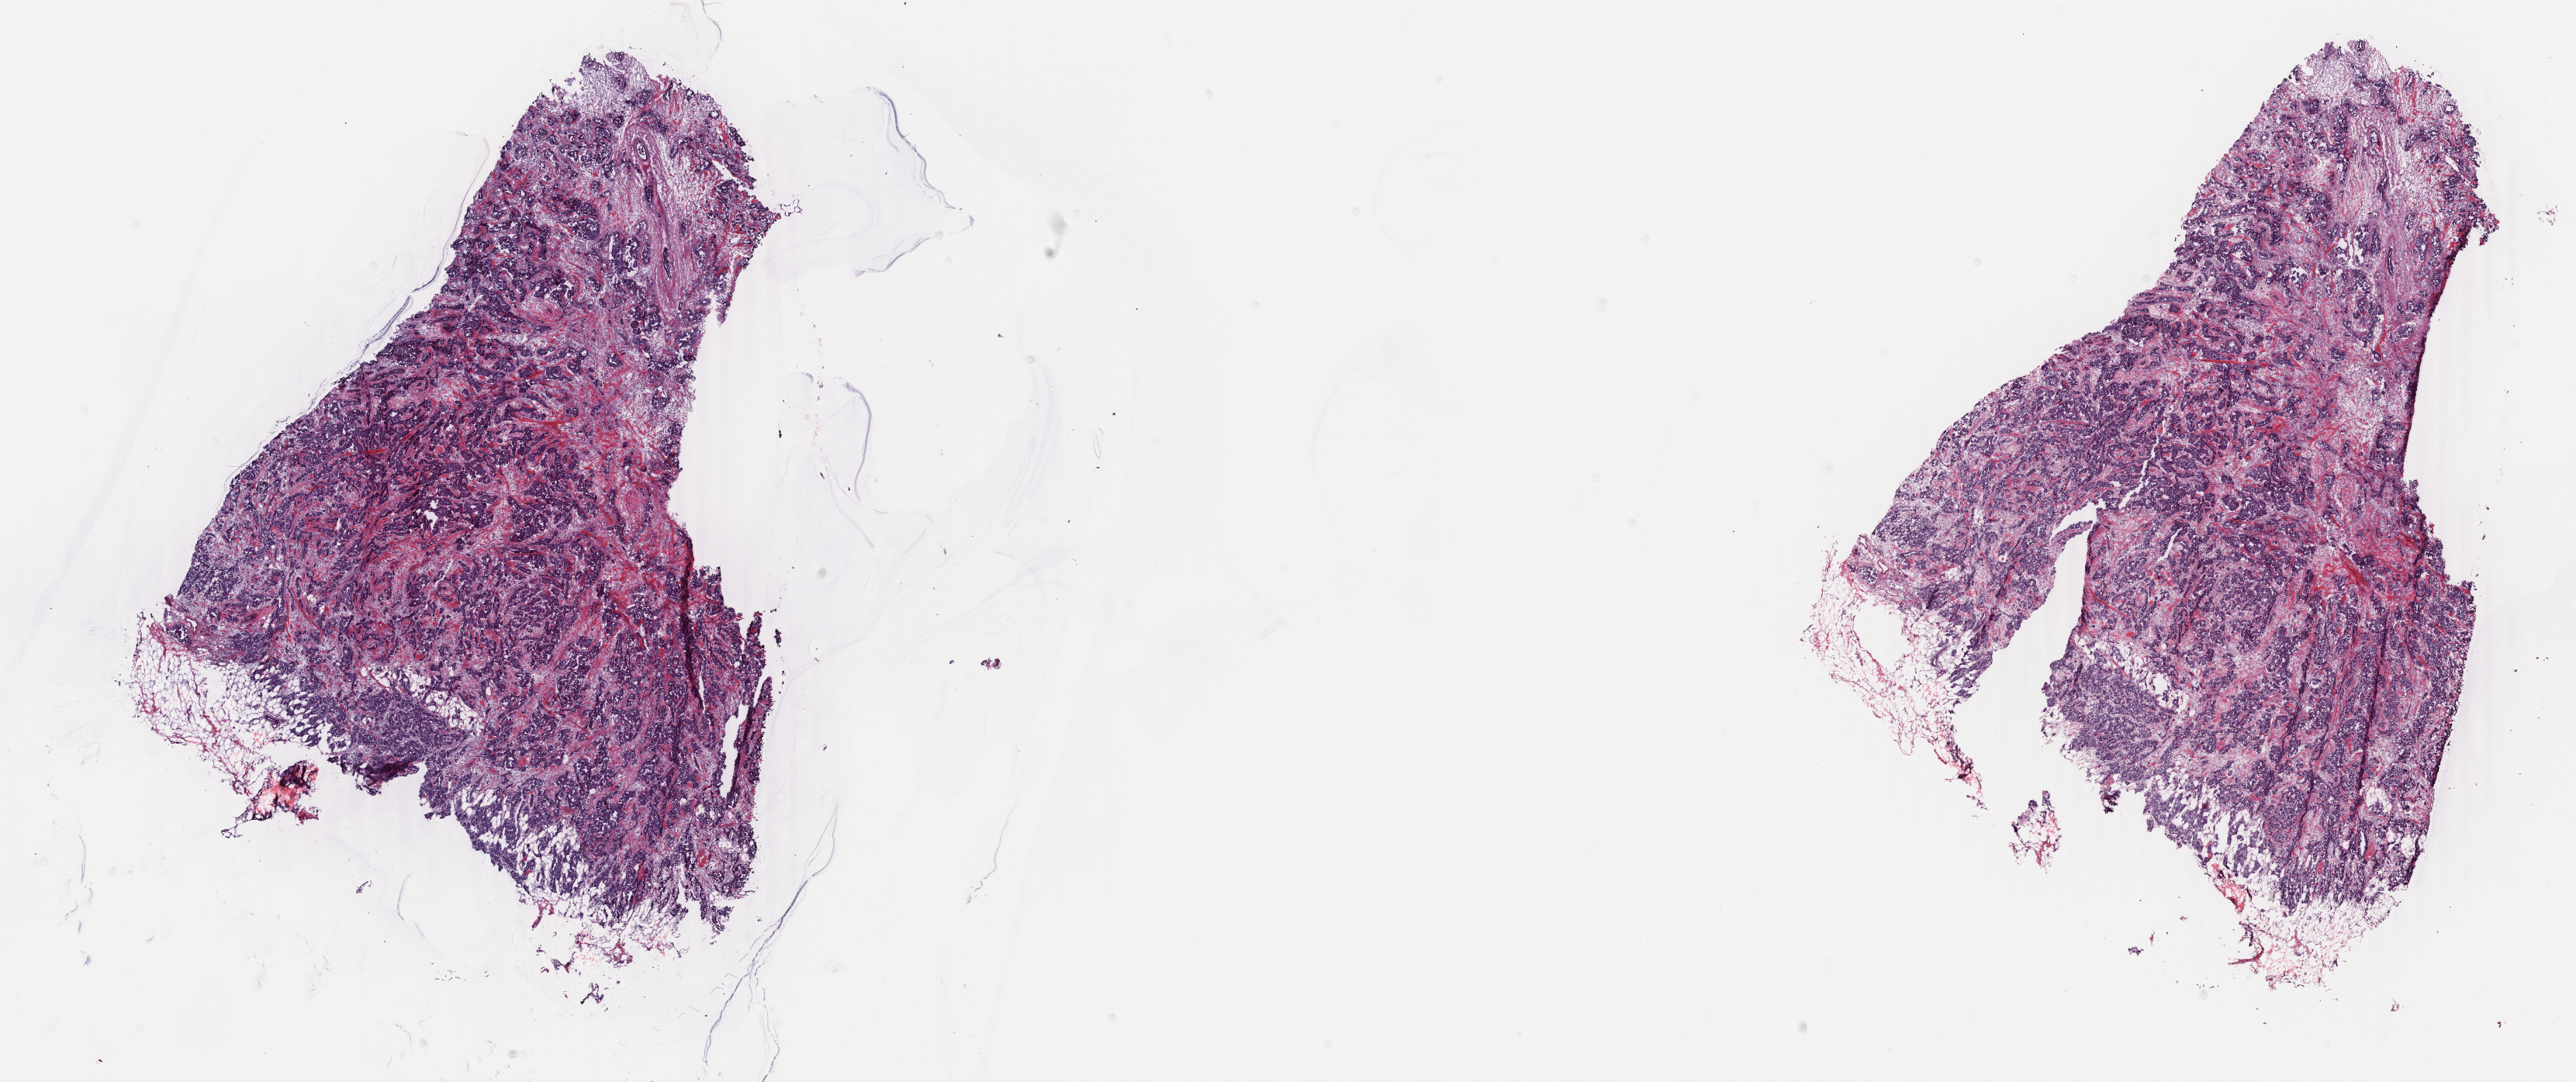
H&E whole-slide image, shown as a low-resolution overview of the whole scanned area (about 26.4 x 11.1 mm); frozen section from the bottom of the tissue portion; sample: primary tumour, breast. Female patient; age at initial diagnosis 45 years. Slide review estimates, as recorded: tumour cells 95%, tumour nuclei 85%, normal cells 0%, stromal cells 5%, necrosis 0%. Inflammatory infiltration, as recorded: lymphocyte infiltration 0%, monocyte infiltration 0%, neutrophil infiltration 0%.
- diagnosis: Infiltrating duct carcinoma, NOS
- laterality: left
- TNM: T2 N2 M0
- AJCC pathologic stage: IIIA
- lymph nodes positive (case pathology): 1 of 14 examined